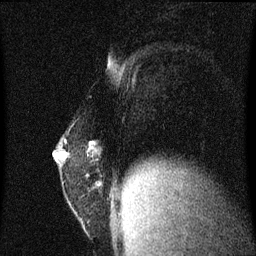
Breast MRI (dynamic contrast-enhanced), one sagittal slice; slice 23 of 60 in the series (ordered by position); dynamic contrast-enhanced series, image 2 of 3 at this slice position (ordered by acquisition); 1.5 T; TE 4.2 ms, TR 8.4 ms; 256 × 256 image matrix. Patient: female, 52 years. Case-level facts recorded for this patient, not image findings: setting: breast cancer imaged before/during neoadjuvant chemotherapy; receptor status: HER2-positive.
Structures marked on this image (semi-automatically segmented with operator editing):
- analysis volume of interest (the breast-tissue region the enhancement analysis was run in; not a lesion): bounding box <54,130,119,191> (left, top, right, bottom; pixels)
- tumour enhancement mask (voxels above the 70 % enhancement threshold inside the analysis volume of interest): <90,142,93,149>